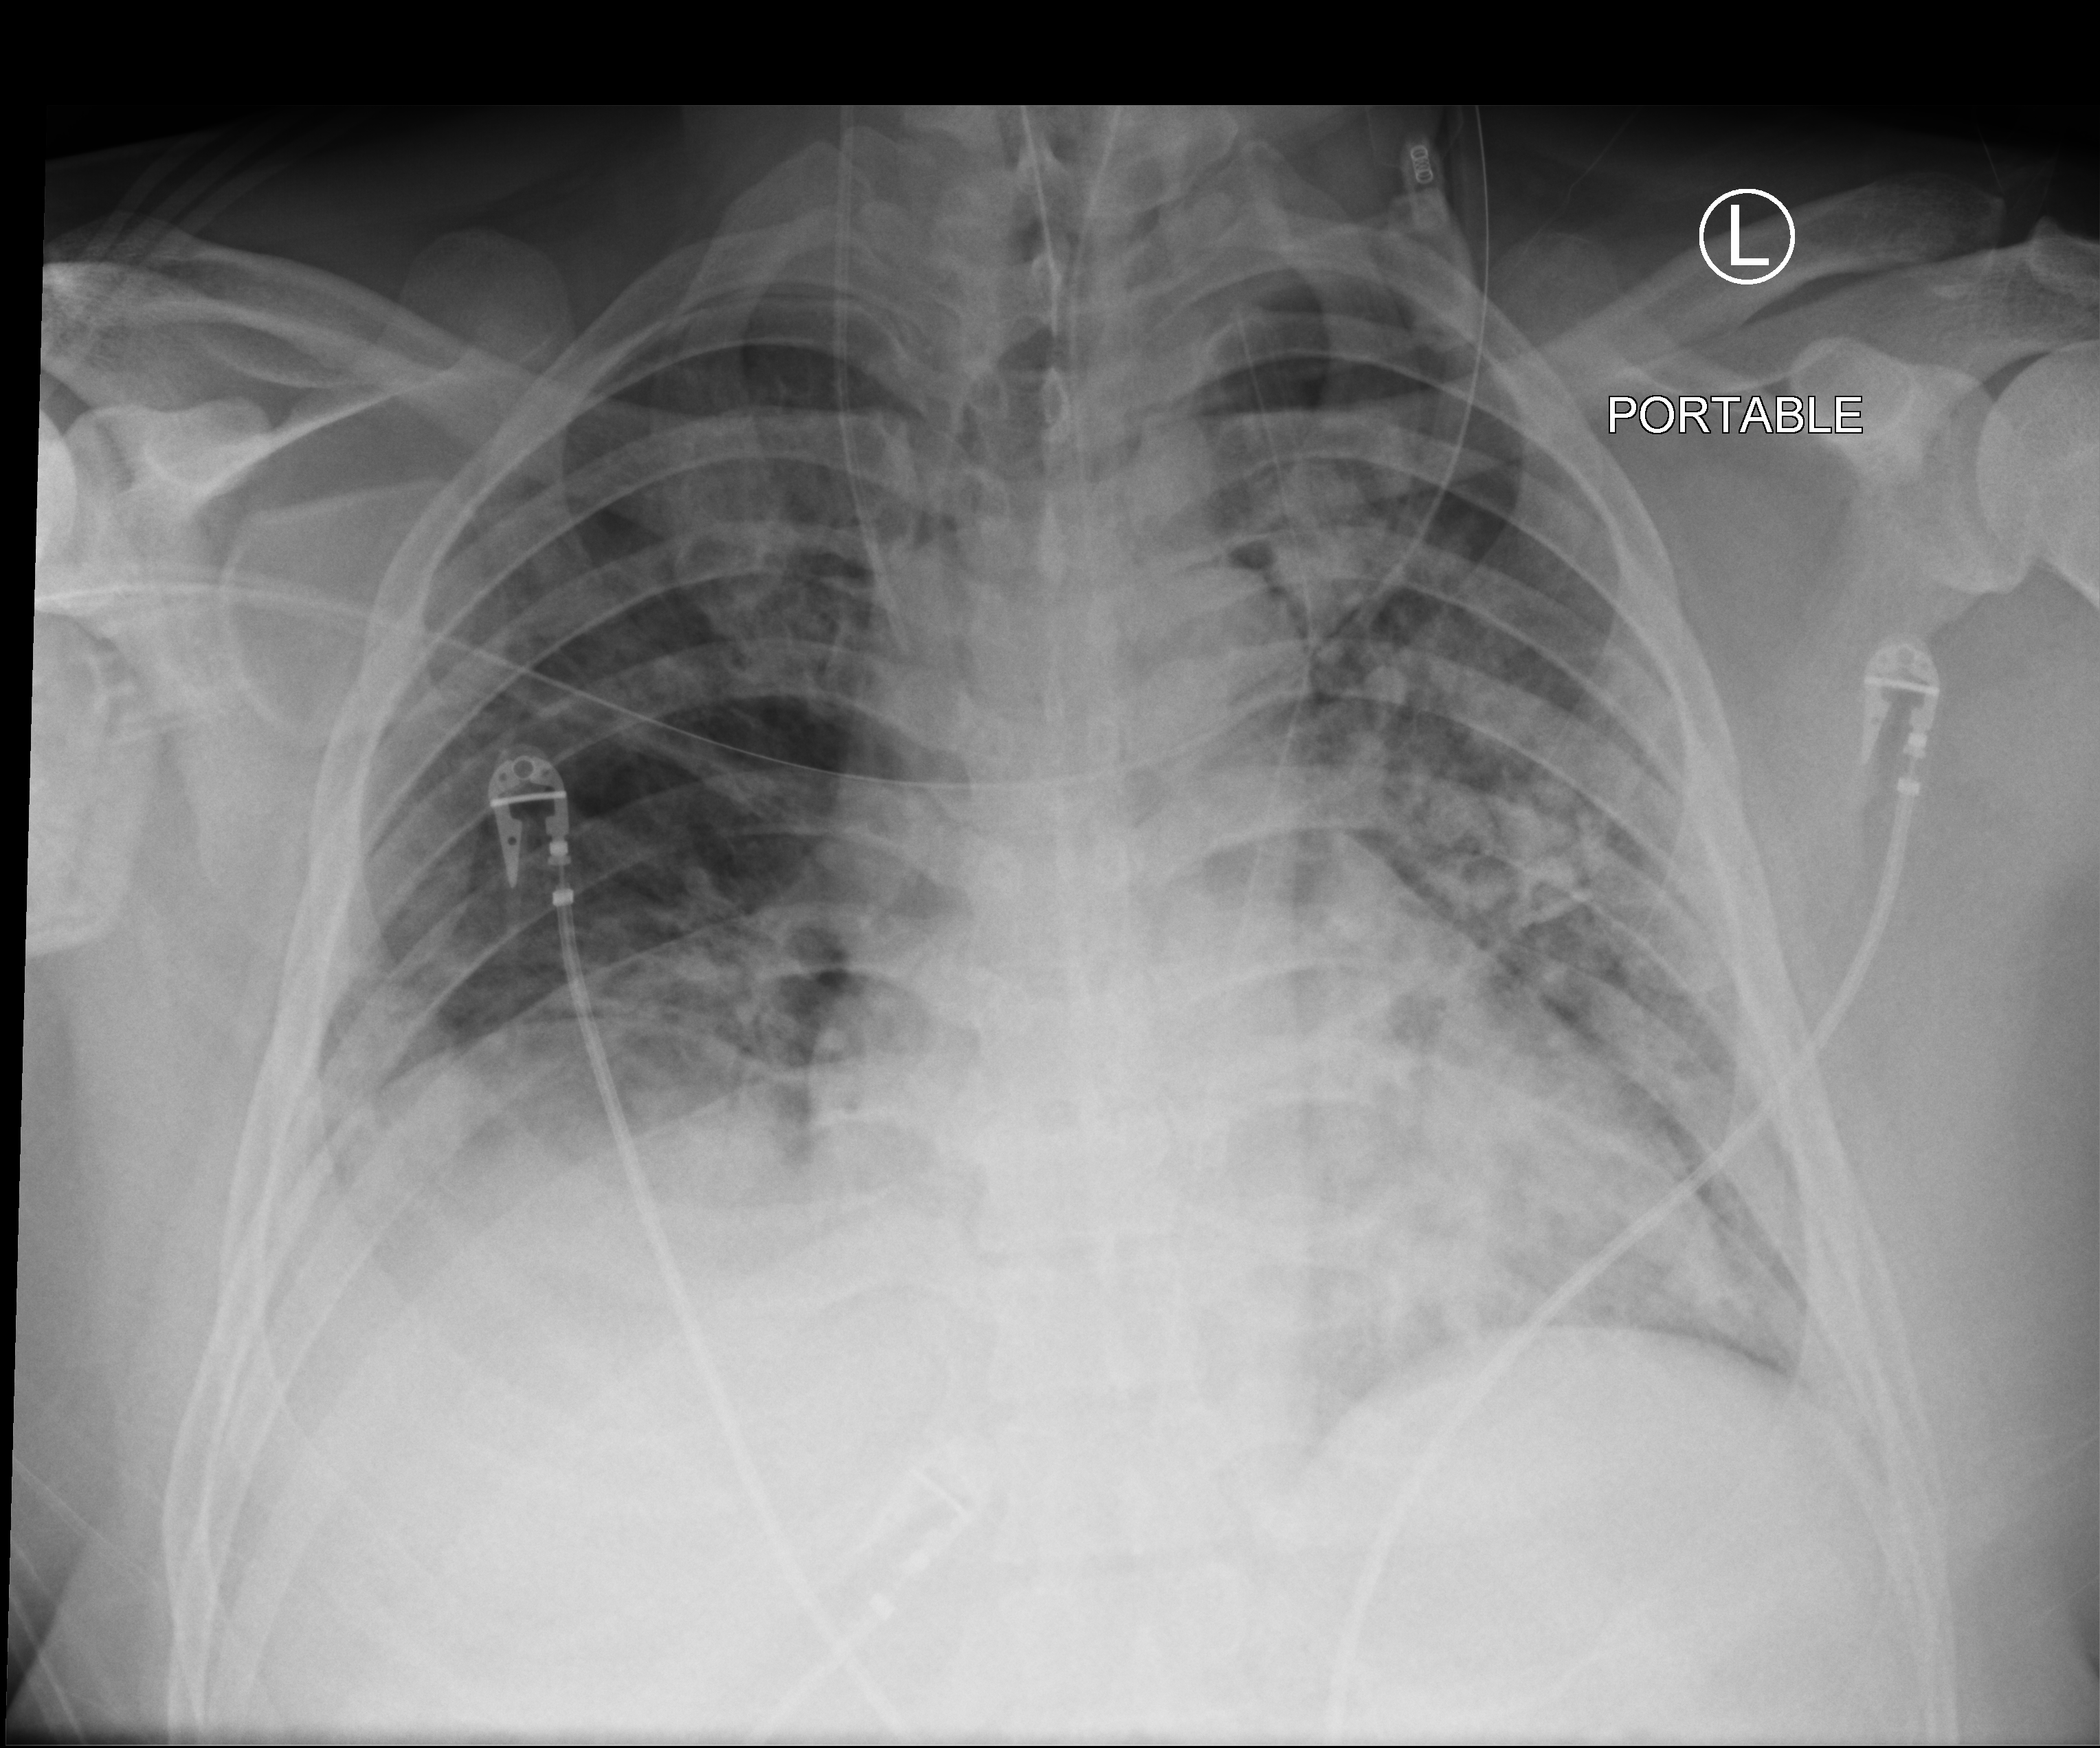
Bedside chest radiograph (computed radiography). Male patient hospitalised with COVID-19, age 18–59 years.
Admission-level facts for this patient (not findings on this image; timing relative to this image not recorded):
- mechanically ventilated during this hospital stay: yes
- admitted to intensive care during this hospital stay: yes